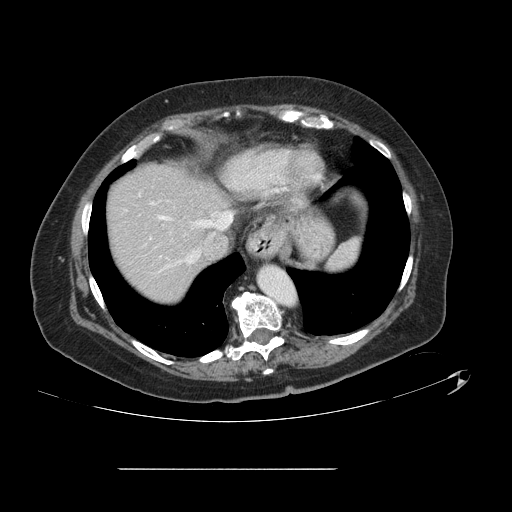
Contrast-enhanced abdominal CT, one axial slice. Position 115 of 148 along the scan axis. Intravenous contrast given. Soft-tissue window (W 400 / L 40 HU). 2.5 mm slice thickness. 512 × 512 image matrix, field of view 439 × 439 mm. Female patient, age 75 years. Case-level facts recorded for this patient, not image findings: diagnosis: colorectal cancer liver metastases, imaged before liver resection; multiple liver metastases: no; largest metastasis: 2.4 cm; disease in both lobes: no.
Structures marked on this image (outlined manually by an expert reader):
- hepatic veins: box from (x=160, y=212) to (x=233, y=263) px
- liver: (x=107, y=166)–(x=228, y=305)
- planned liver remnant (the part of the liver to remain after resection): (x=107, y=166)–(x=227, y=304)